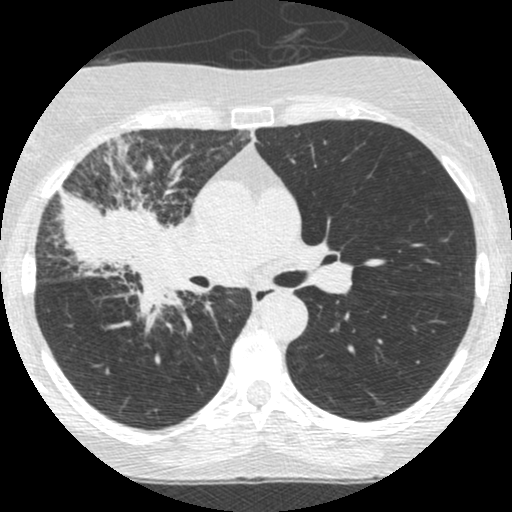
Low-dose screening chest CT, one axial slice. Position 153 of 253 along the scan axis. Reconstruction kernel STANDARD. 120 kVp. Lung window (W 1500 / L -600 HU). 1.25 mm slice thickness. 512 × 512 image matrix, field of view 294 × 294 mm.
Outlined on this slice (expert manual segmentation):
- lesion 2 (tumor, hilum of right lung): bounding box (x1, y1, x2, y2) in pixels: (60, 191, 186, 330)